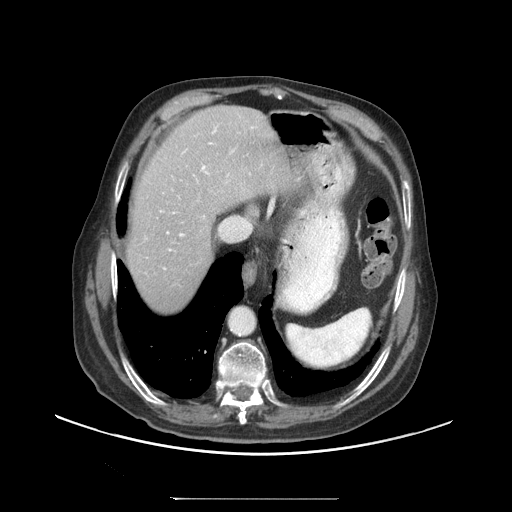
Contrast-enhanced abdominal CT (liver protocol), one axial slice. Reconstruction kernel STANDARD. Soft-tissue window (W 400 / L 40 HU). 2.5 mm slice thickness. 512 × 512 image matrix, field of view 450 × 450 mm. Case-level facts recorded for this patient, not image findings: diagnosis: hepatocellular carcinoma (patient treated with transarterial chemoembolisation; whether this scan precedes or follows treatment is not stated here); TNM stage (as recorded): Stage-IIIC; Child-Pugh class: A; tumour differentiation: well differentiated; tumour nodularity: uninodular.
Annotated regions visible in this slice (semi-automatically segmented with operator editing):
- abdominal aorta: bounding box <231,307,256,334> (left, top, right, bottom; pixels)
- liver parenchyma outside the tumour (the mass and vessels are separate outlines, so this box may not span the whole liver): <126,106,300,312>
- liver vessels: <160,127,254,269>